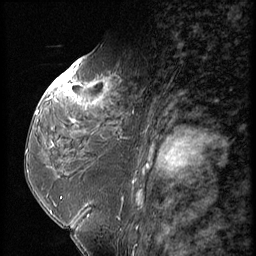
Breast MRI (dynamic contrast-enhanced), one sagittal slice; slice 31 of 56 in the series (ordered by position); dynamic contrast-enhanced series, image 2 of 3 at this slice position (ordered by acquisition); 1.5 T; TE 4.2 ms, TR 9 ms; 2.5 mm slice thickness; 256 × 256 image matrix, field of view 180 × 180 mm. Patient: female, 59 years. From the clinical record (not read from this slice): setting: breast cancer imaged before/during neoadjuvant chemotherapy; receptor status: HER2-positive.
Annotated regions visible in this slice (semi-automatic segmentation, software-assisted and operator-edited):
- analysis volume of interest (the breast-tissue region the enhancement analysis was run in; not a lesion): bounding box (x1, y1, x2, y2) in pixels: (44, 66, 151, 135)
- tumour enhancement mask (voxels above the 140 % enhancement threshold inside the analysis volume of interest): (51, 69, 107, 98)